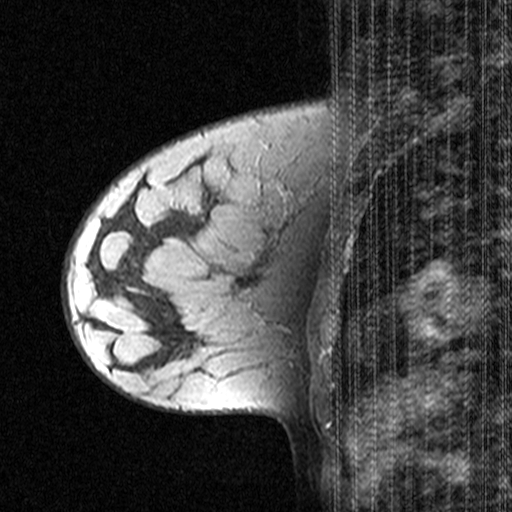
Breast MRI (dynamic contrast-enhanced), one sagittal slice; slice 13 of 44 in the series (ordered by position); dynamic contrast-enhanced study with each time point stored as its own series, time point 2 of 3 at this slice position (early post-contrast, ordered by acquisition time); 1.5 T; TE 4.5 ms, TR 11 ms; 3 mm slice thickness; 512 × 512 image matrix, field of view 200 × 200 mm. Female patient, age 28 years. From the clinical record (not read from this slice): setting: breast cancer imaged before/during neoadjuvant chemotherapy; receptor status: HR-positive, HER2-negative.
Annotated regions visible in this slice (semi-automatic segmentation, software-assisted and operator-edited):
- analysis volume of interest (the breast-tissue region the enhancement analysis was run in; not a lesion): bounding box [x1, y1, x2, y2] px = [64, 182, 151, 283]
- tumour enhancement mask (voxels above the 90 % enhancement threshold inside the analysis volume of interest): [105, 235, 109, 239]